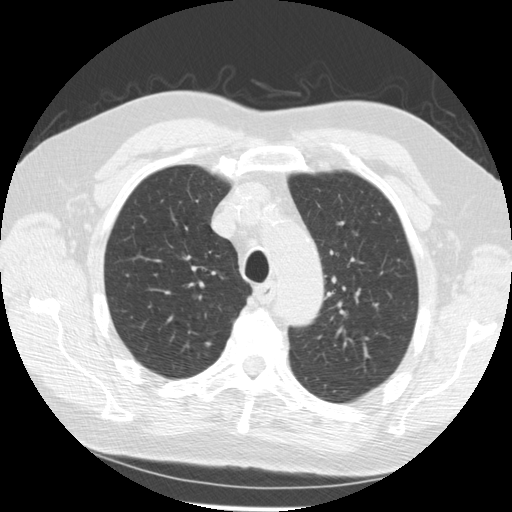
Low-dose screening chest CT, one axial slice; position 203 of 259 along the scan axis; 120 kVp; lung window (W 1500 / L -600 HU); 2.5 mm slice thickness; 512 × 512 image matrix.
Structures marked on this image (manually delineated by an expert):
- lesion 1 (nodule, upper lobe of right lung): bounding box (x1, y1, x2, y2) in pixels: (205, 341, 213, 348)